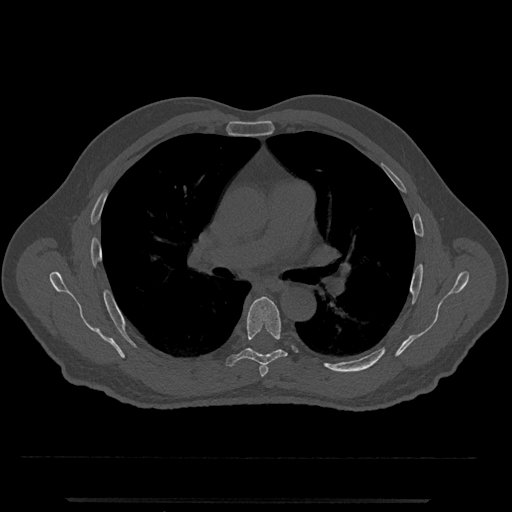
CT including the spine, one axial slice. Position 740 of 797 along the scan axis. 120 kVp. Bone window (W 1800 / L 400 HU). 0.5 mm slice thickness. 512 × 512 image matrix, field of view 419 × 419 mm. Patient: male, 63 years. Case-level facts recorded for this patient, not image findings: primary cancer: prostate.
Outlined on this slice (semi-automatically segmented with operator editing):
- T5 vertebra: bounding box [x1, y1, x2, y2] px = [259, 364, 269, 377]
- T6 vertebra: [225, 296, 288, 367]